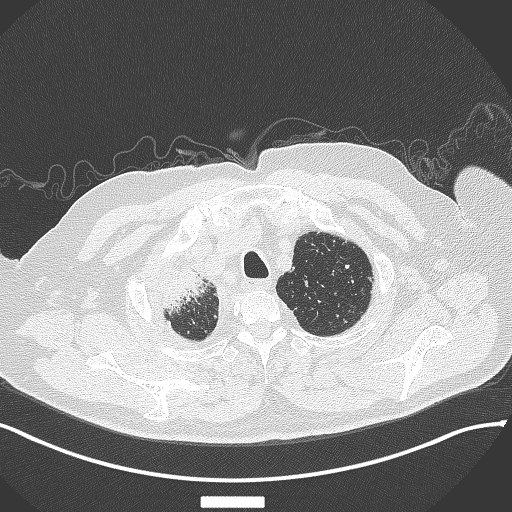
Chest CT, one axial slice; position 325 of 384 along the scan axis; reconstruction kernel B70f; 120 kVp; lung window (W 1500 / L -600 HU); 512 × 512 image matrix, field of view 400 × 400 mm. Patient: male, 69 years. From the clinical record (not read from this slice): clinical TNM (as recorded): T4 N3 M1.
Structures marked on this image (rectangle marked by the reading radiologist):
- lung tumour (recorded histology: adenocarcinoma): box from (x=160, y=250) to (x=215, y=313) px